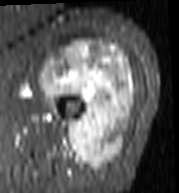
MRI of an extremity soft-tissue mass, one axial slice; slice 72 of 103 in the series (ordered by position); STIR; MR volume resampled by the dataset authors to the PET/CT grid (not the native acquisition matrix); 3.27 mm slice thickness; 179 × 193 image matrix, field of view 175 × 188 mm. Female patient. From the clinical record (not read from this slice): histological type: undifferentiated – high grade; grade: high; site of the primary tumour: left thigh.
Annotated regions visible in this slice (expert contour drawn on MRI and transferred to this co-registered scan by the dataset authors):
- gross tumour volume including surrounding oedema: box from (x=41, y=41) to (x=135, y=170) px
- gross tumour volume (mass): (x=41, y=41)–(x=135, y=170)